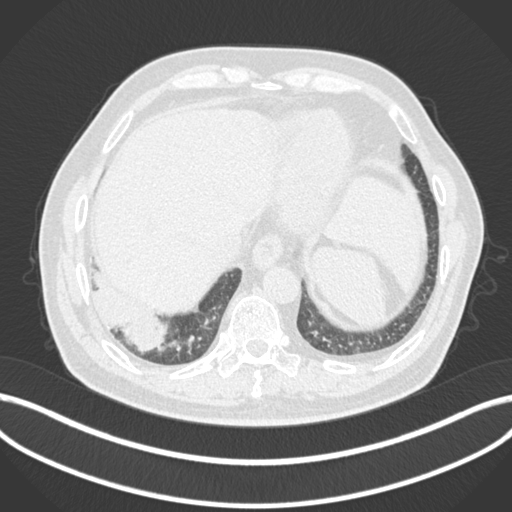
Chest CT, one axial slice. Slice 22 of 200 in the series (ordered by position). Reconstruction kernel B30f. 120 kVp. Lung window (W 1500 / L -600 HU). 512 × 512 image matrix. Male patient, age 59 years.
Outlined on this slice (bounding box drawn by a radiologist):
- lung tumour (recorded histology: adenocarcinoma): box from (x=85, y=268) to (x=166, y=355) px